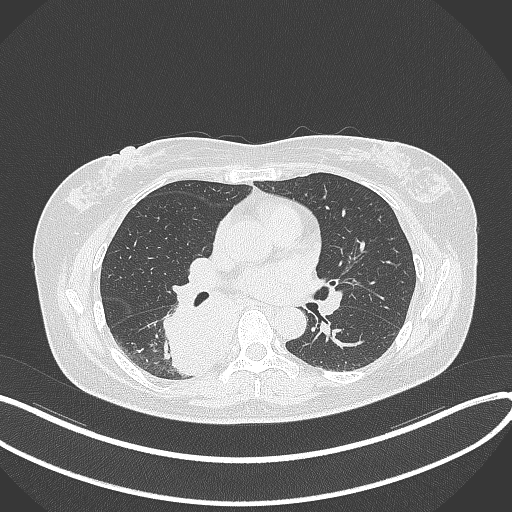
Chest CT, one axial slice. Slice 192 of 331 in the series (ordered by position). Reconstruction kernel B70f. 120 kVp. Lung window (W 1500 / L -600 HU). 1 mm slice thickness. 512 × 512 image matrix, field of view 400 × 400 mm. Patient: female, 54 years. From the clinical record (not read from this slice): clinical TNM (as recorded): T4 N0 M0.
Outlined on this slice (rectangle marked by the reading radiologist):
- lung tumour (recorded histology: adenocarcinoma): bounding box <161,291,239,376> (left, top, right, bottom; pixels)